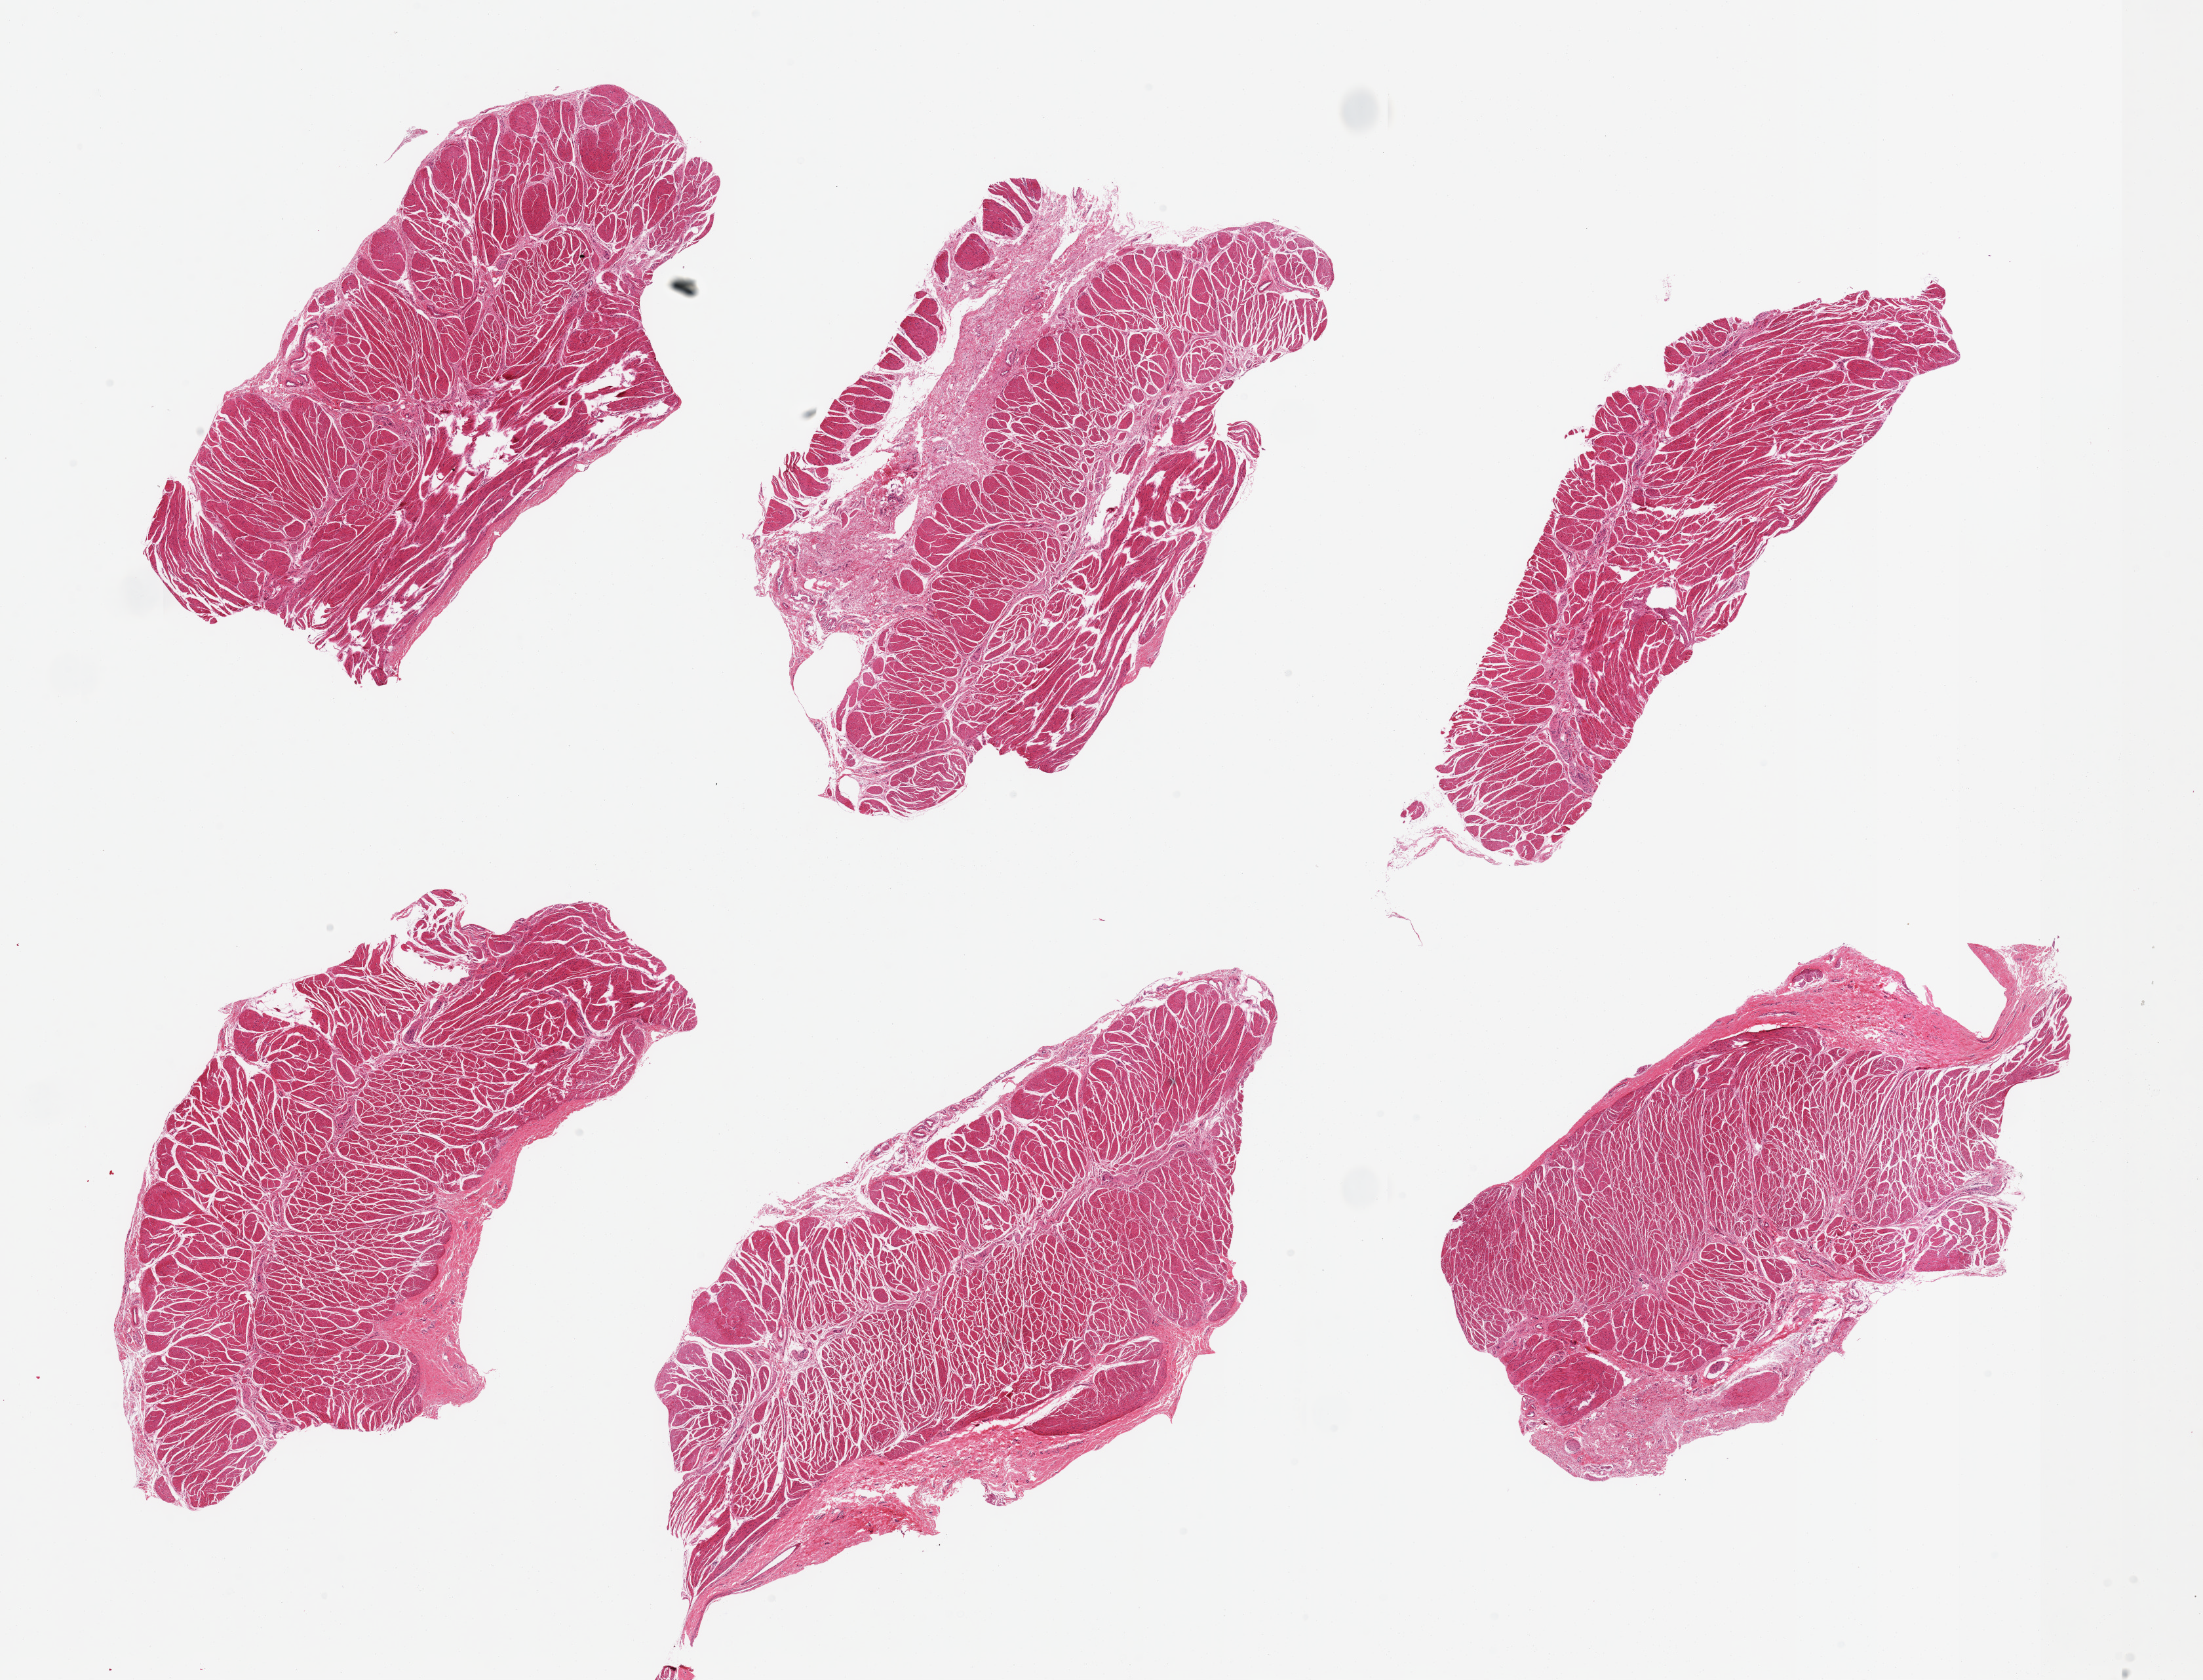
H&E whole-slide image, brightfield, whole scanned area (about 26.6 x 20.3 mm, from a 20x scan) shown as a low-resolution overview; PAXgene-fixed, paraffin-embedded tissue; sampled site (target tissue): esophageal muscle; donor tissue sample.
Reviewer comment on this tissue sample: 6 pieces, confirmed target muscularis.